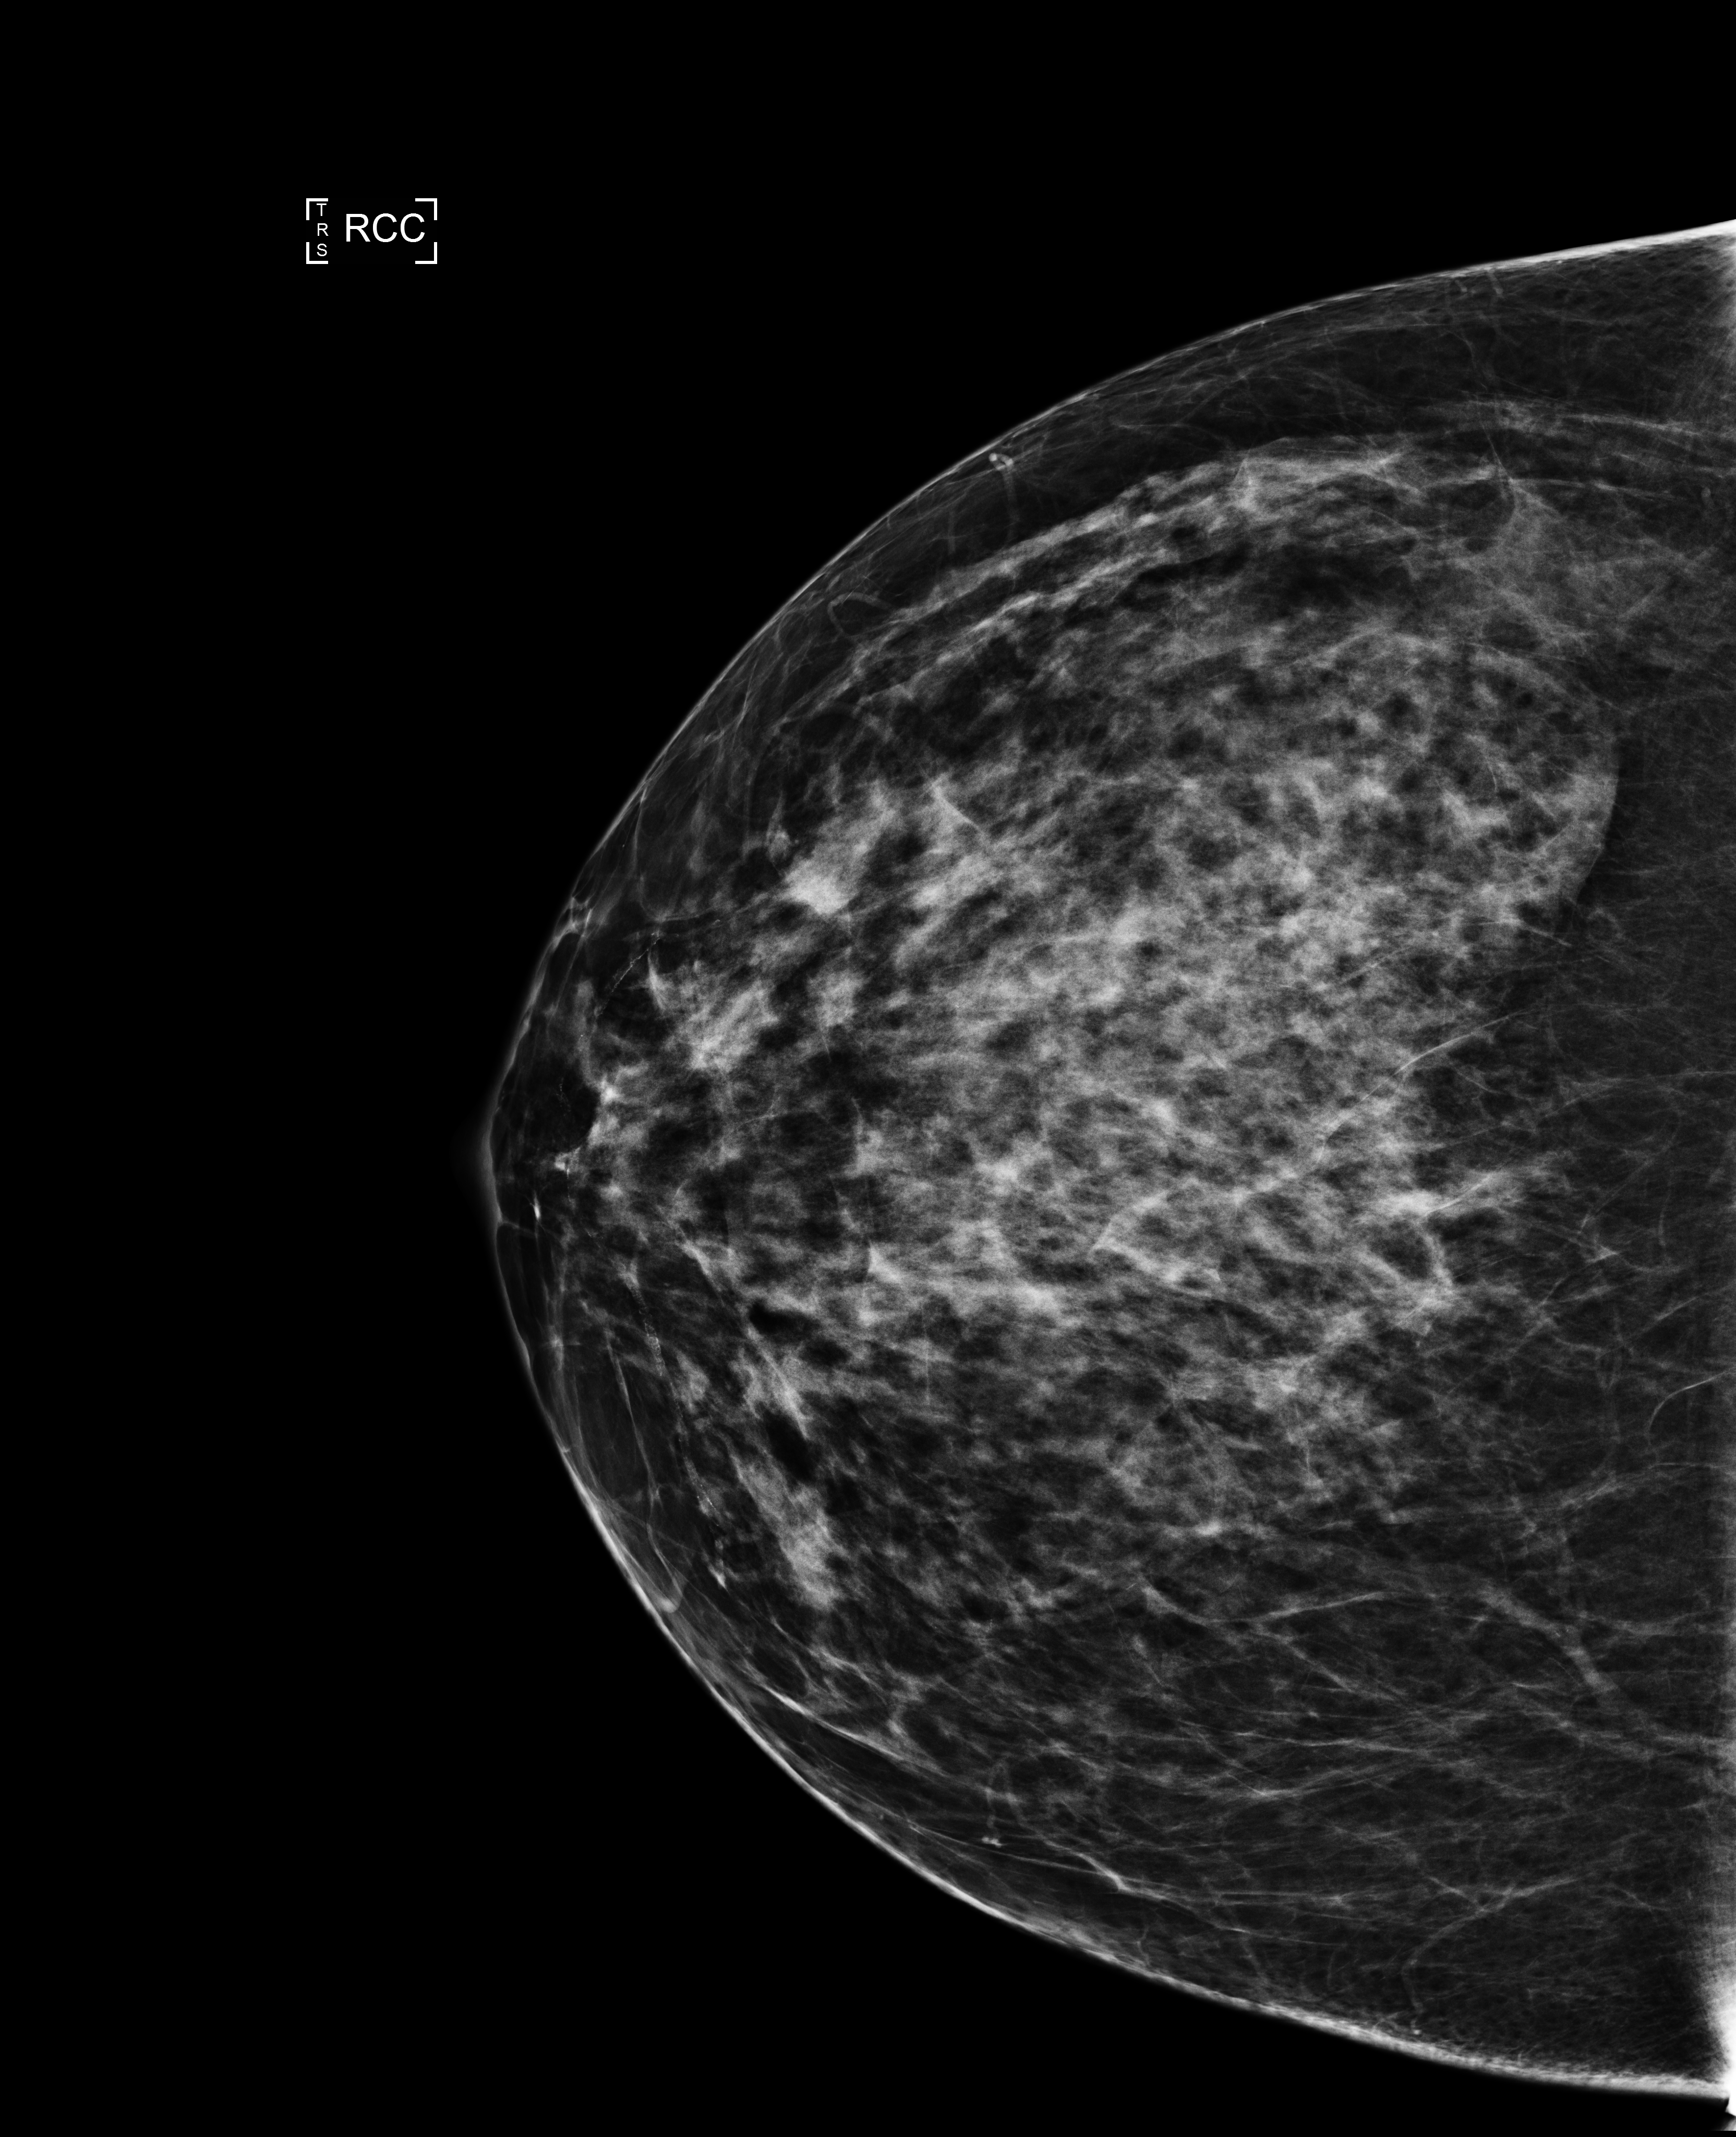
Screening examination. Patient: female, 45 years.
Image type: full-field digital mammogram. Breast: right. Projection: craniocaudal (CC) view.